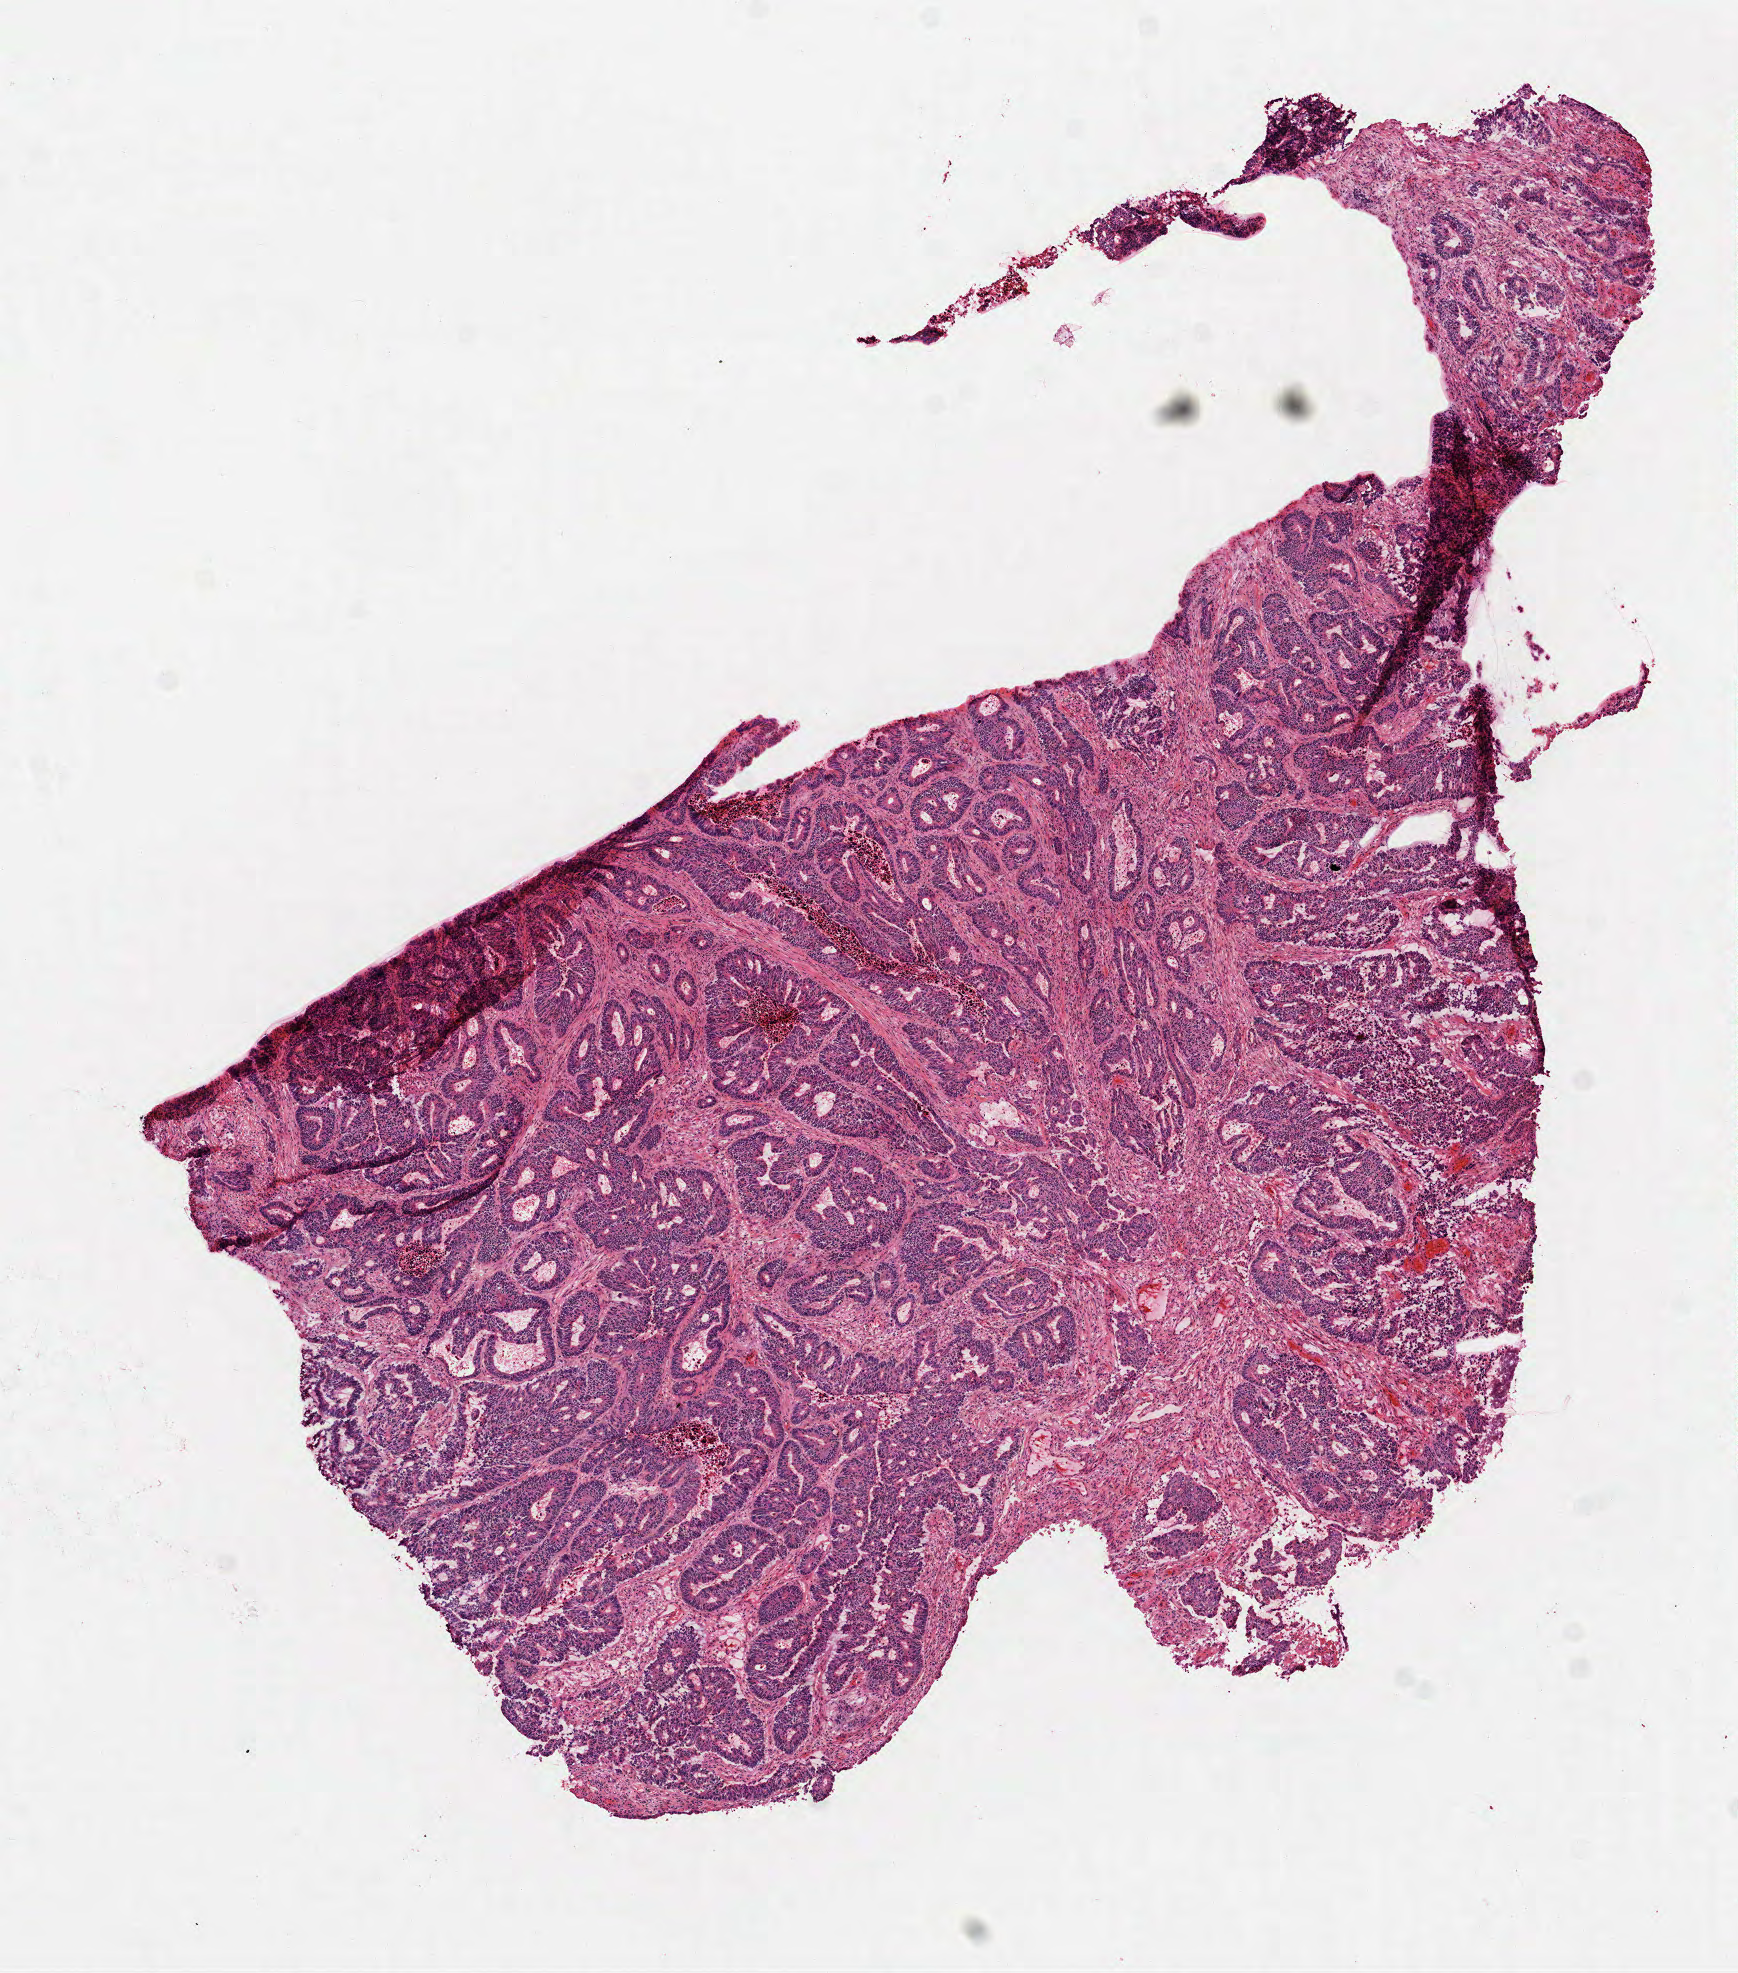
H&E-stained whole-slide image — a low-resolution overview of the entire scanned area, about 7.0 x 8.0 mm (slide scanned at 40x), frozen section from the top of the tissue portion, sample: primary tumour, colon. Male patient; age at initial diagnosis 81 years. Composition of this section per pathologist review: tumour cells 85%, tumour nuclei 80%, normal cells 0%, stromal cells 10%, necrosis 5%.
Diagnosis: Adenocarcinoma, NOS (sigmoid colon). AJCC pathologic stage: IIIB.